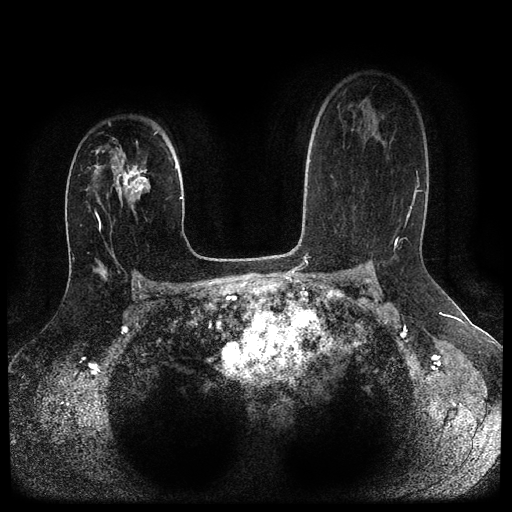
Breast MRI (dynamic contrast-enhanced, multi-phase), one axial slice; slice 68 of 116 in the series (ordered by position); dynamic contrast-enhanced series, time point 2 of 5 at this slice position (early post-contrast); 1.5 T; TE 2.6 ms, TR 5.4 ms; 2 mm slice thickness; 512 × 512 image matrix, field of view 340 × 340 mm. Female patient, age 29 years.
Annotated regions visible in this slice (semi-automatically segmented with operator editing):
- breast lesion (labelled 'tumour' in the annotation; benign lesions carry a separate 'benign' label): bounding box (x1, y1, x2, y2) in pixels: (112, 160, 151, 212)